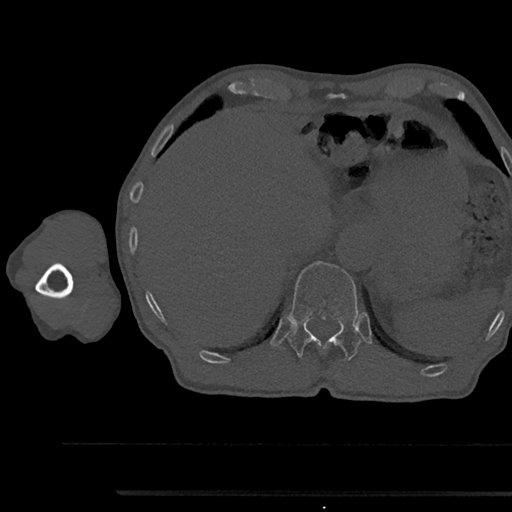
CT including the spine, one axial slice. Position 725 of 797 along the scan axis. 120 kVp. Bone window (W 1800 / L 400 HU). 512 × 512 image matrix, field of view 367 × 367 mm. Male patient, age 79 years. From the clinical record (not read from this slice): primary cancer: prostate.
Structures marked on this image (semi-automatically segmented with operator editing):
- T12 vertebra: bounding box (x1, y1, x2, y2) in pixels: (288, 261, 361, 360)